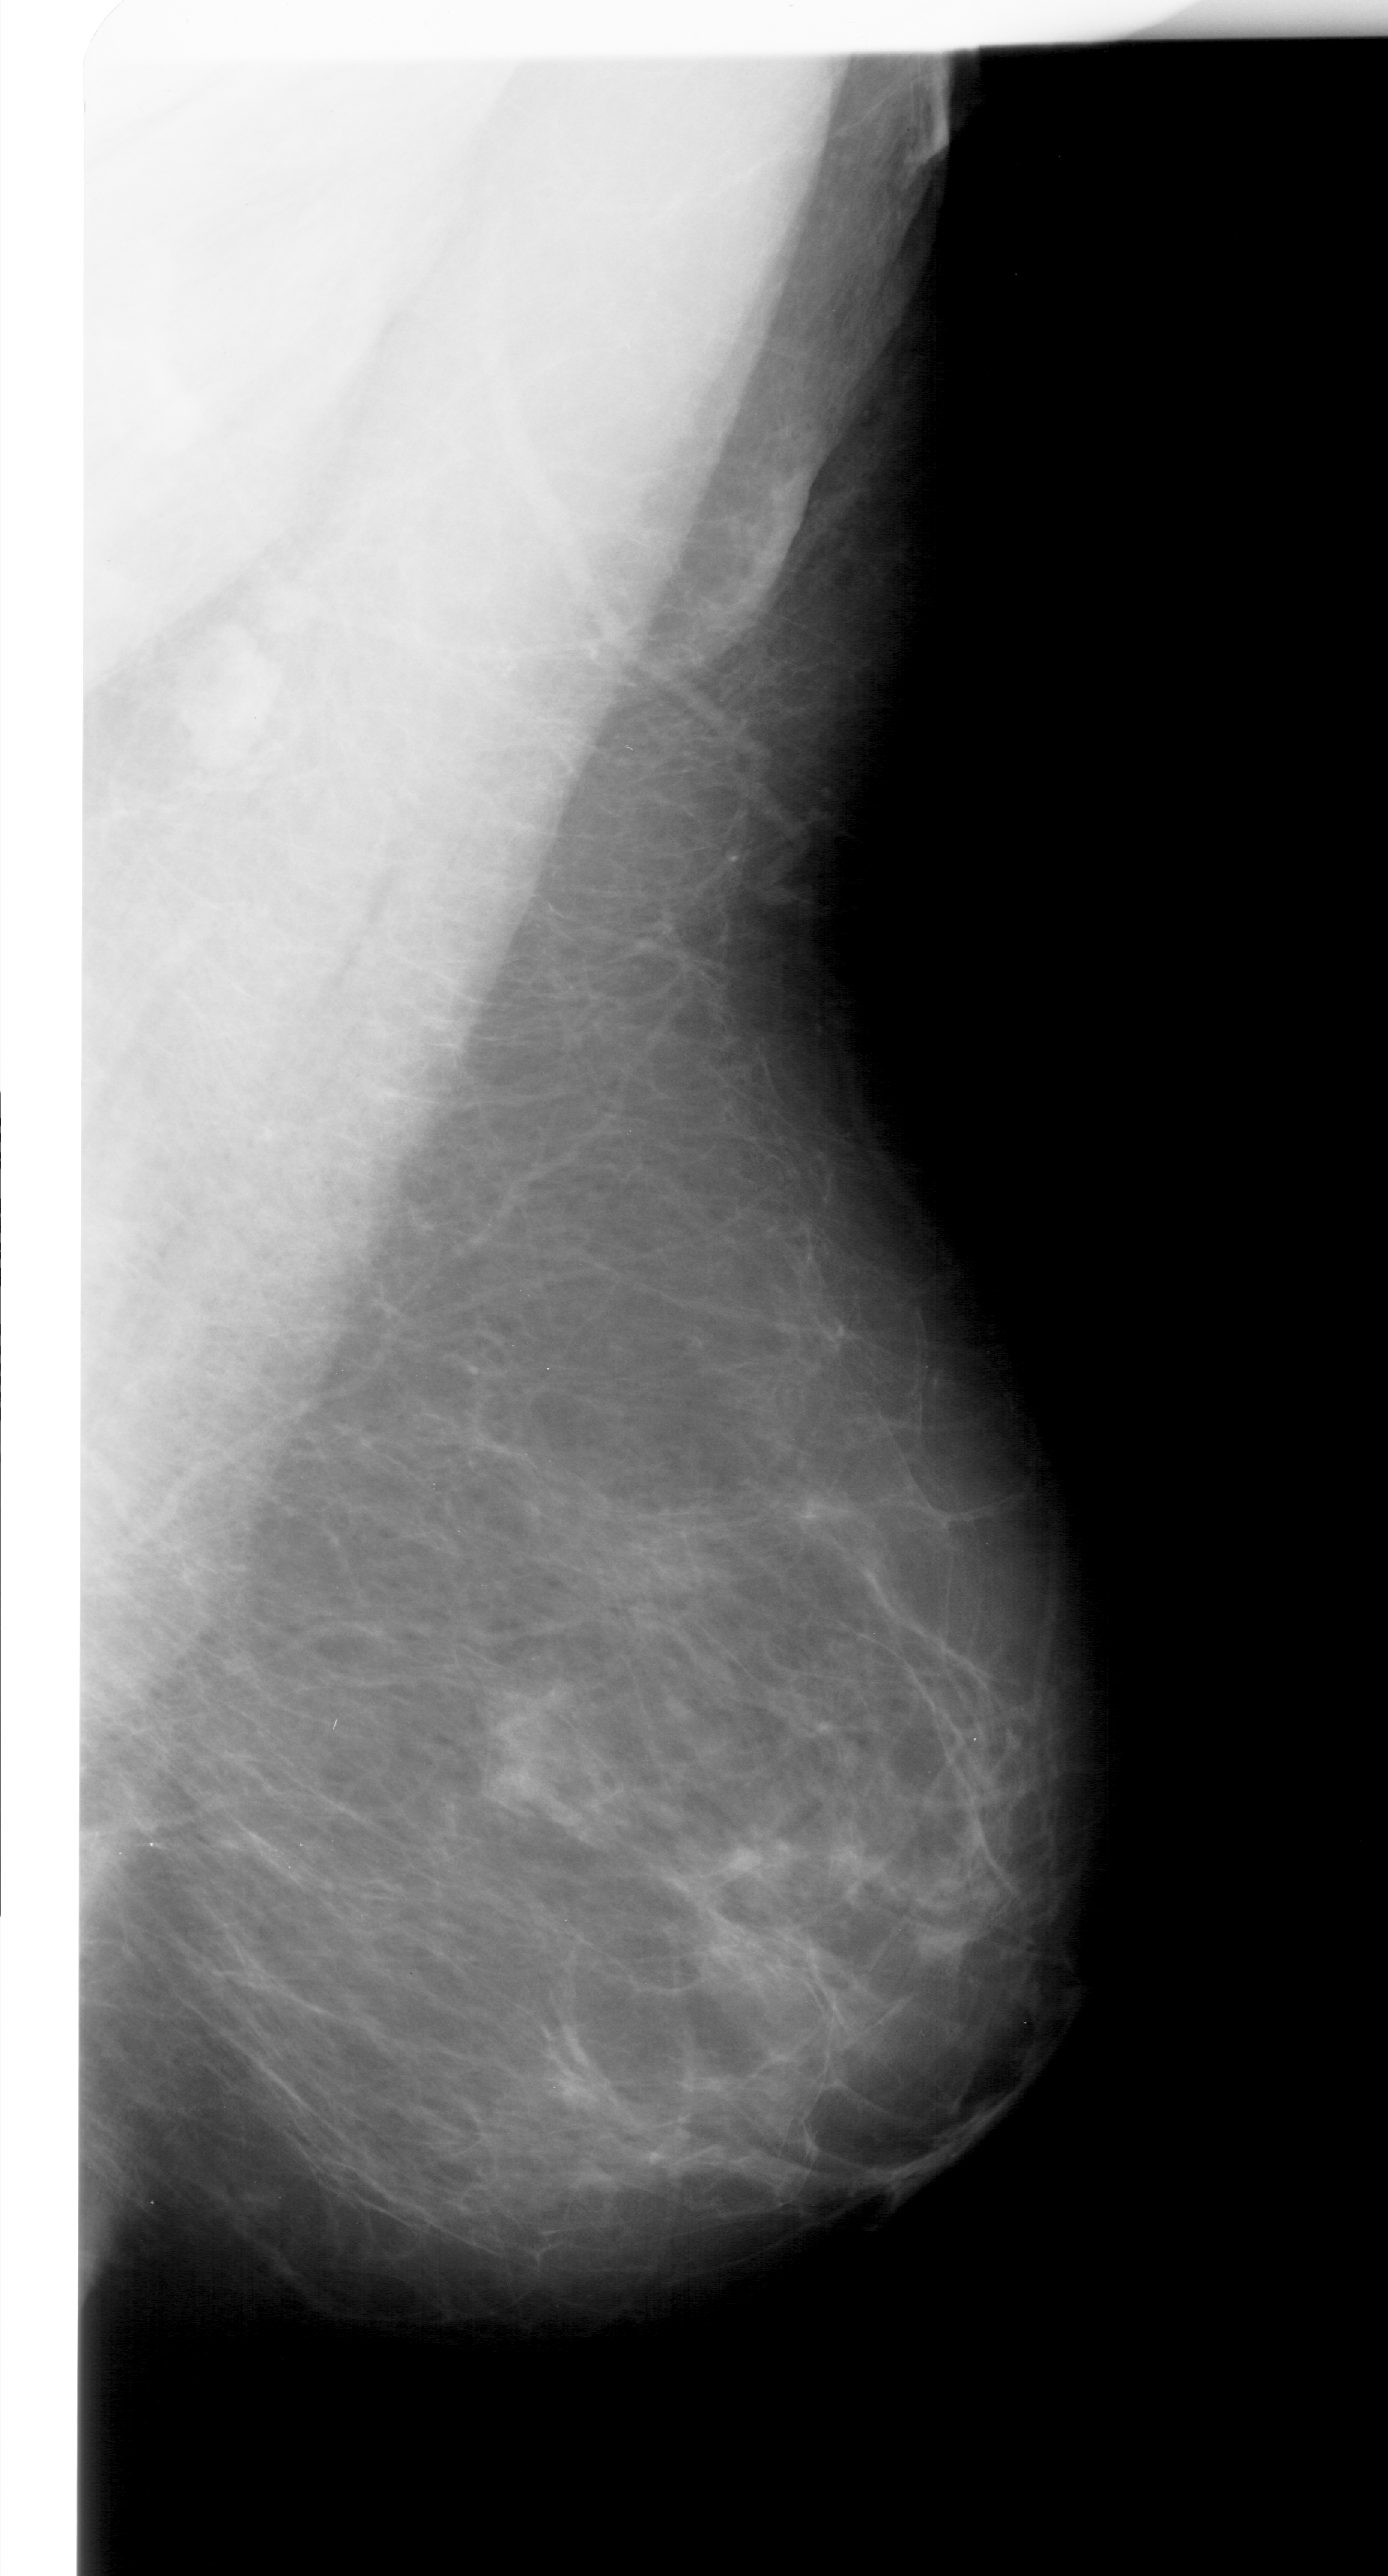
Scanned film-screen mammogram, right breast, mediolateral oblique (MLO) view, breast composition: scattered fibroglandular densities (BI-RADS density category 2 of 4).
Mass, shape focal asymmetric density, margins ill defined; BI-RADS assessment category 4; pathology result (as recorded, not read from the image): benign.